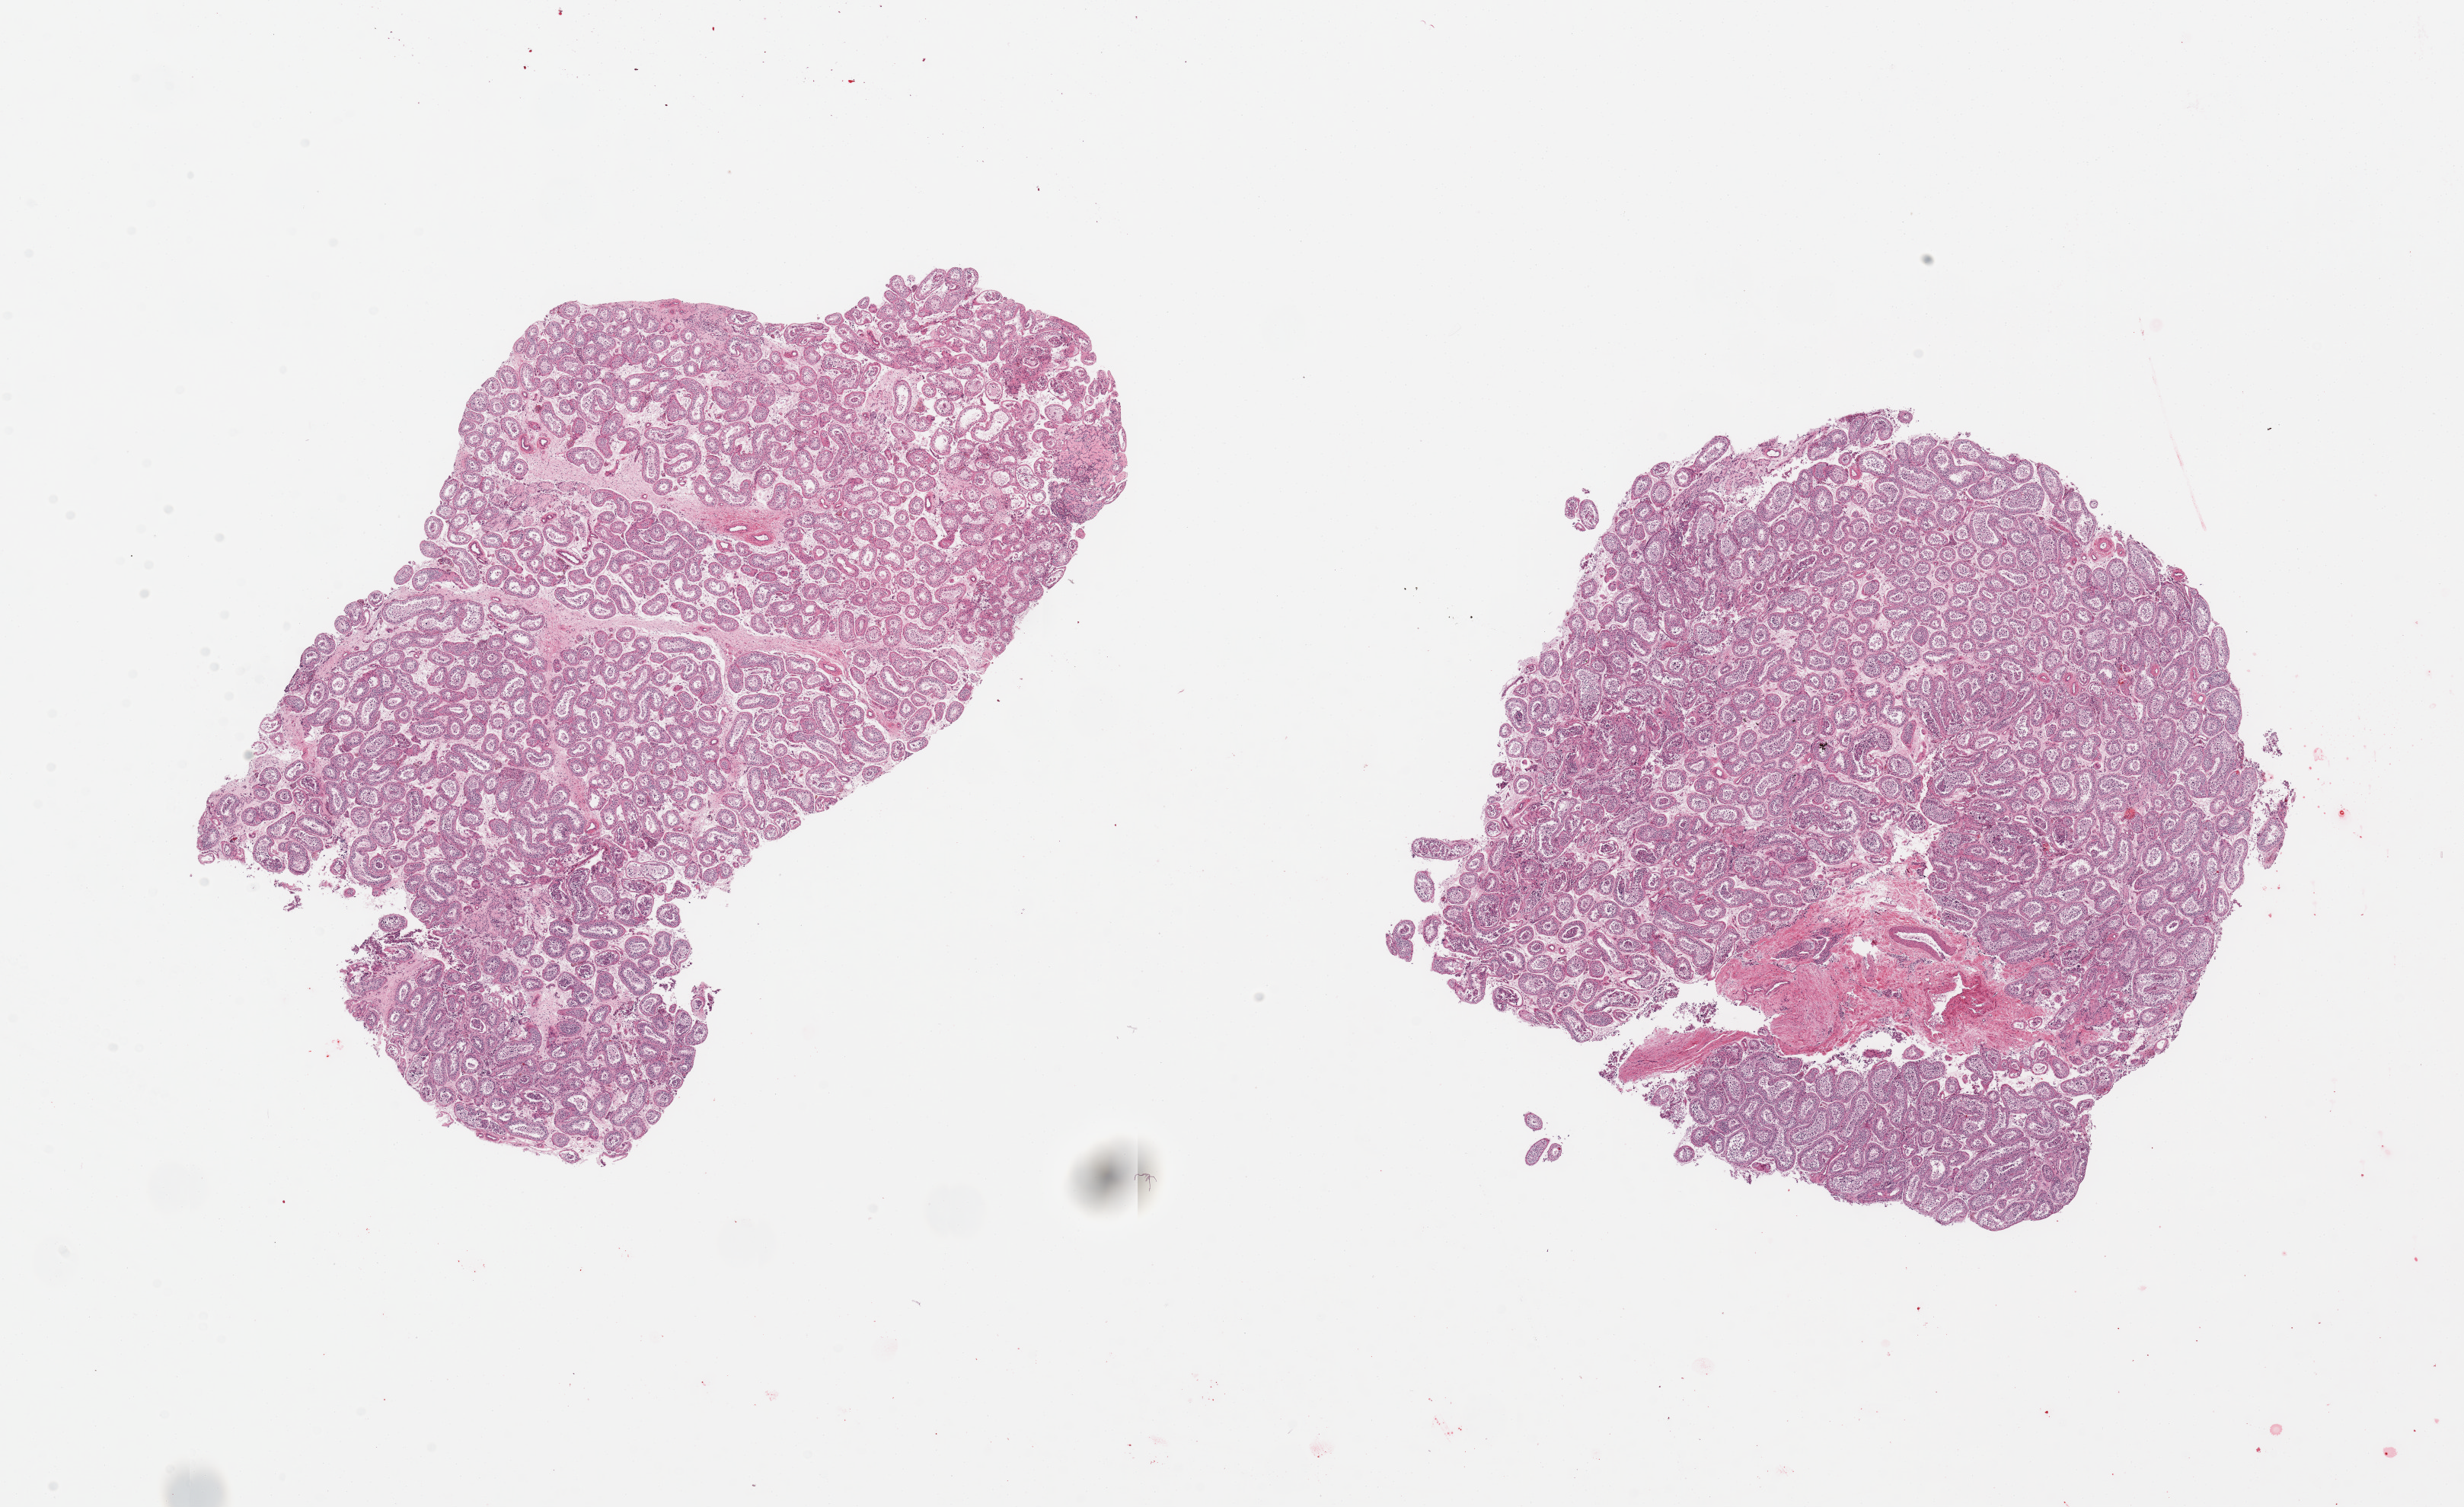
H&E whole-slide image, a low-resolution overview of the entire scanned area, about 25.6 x 15.7 mm (from a 20x scan). PAXgene-fixed paraffin-embedded (PFPE) section. Section of testis (target tissue). Tissue donor sample. Donor: male.
- pathologist's review note for this sample: 2 pieces; spermatogenesis is present, focal hyalinization of tubules